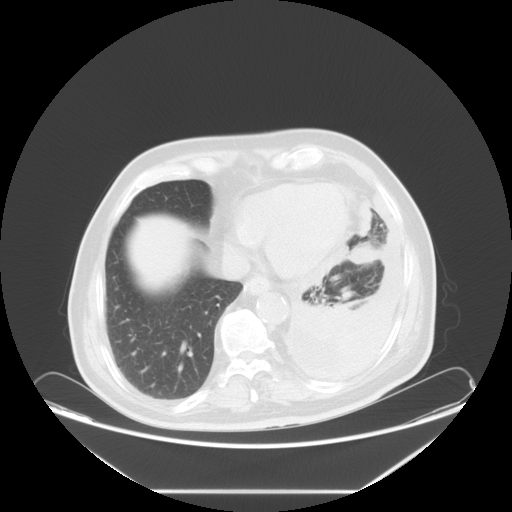
Chest CT, one axial slice; position 20 of 63 along the scan axis; reconstruction kernel STANDARD; 120 kVp; lung window (W 1500 / L -600 HU); 512 × 512 image matrix, field of view 448 × 448 mm. Patient: male, 67 years. Case-level facts recorded for this patient, not image findings: clinical TNM (as recorded): T1b N1 M1a.
Outlined on this slice (bounding box drawn by a radiologist):
- lung tumour (recorded histology: small cell carcinoma): bounding box <349,236,383,274> (left, top, right, bottom; pixels)